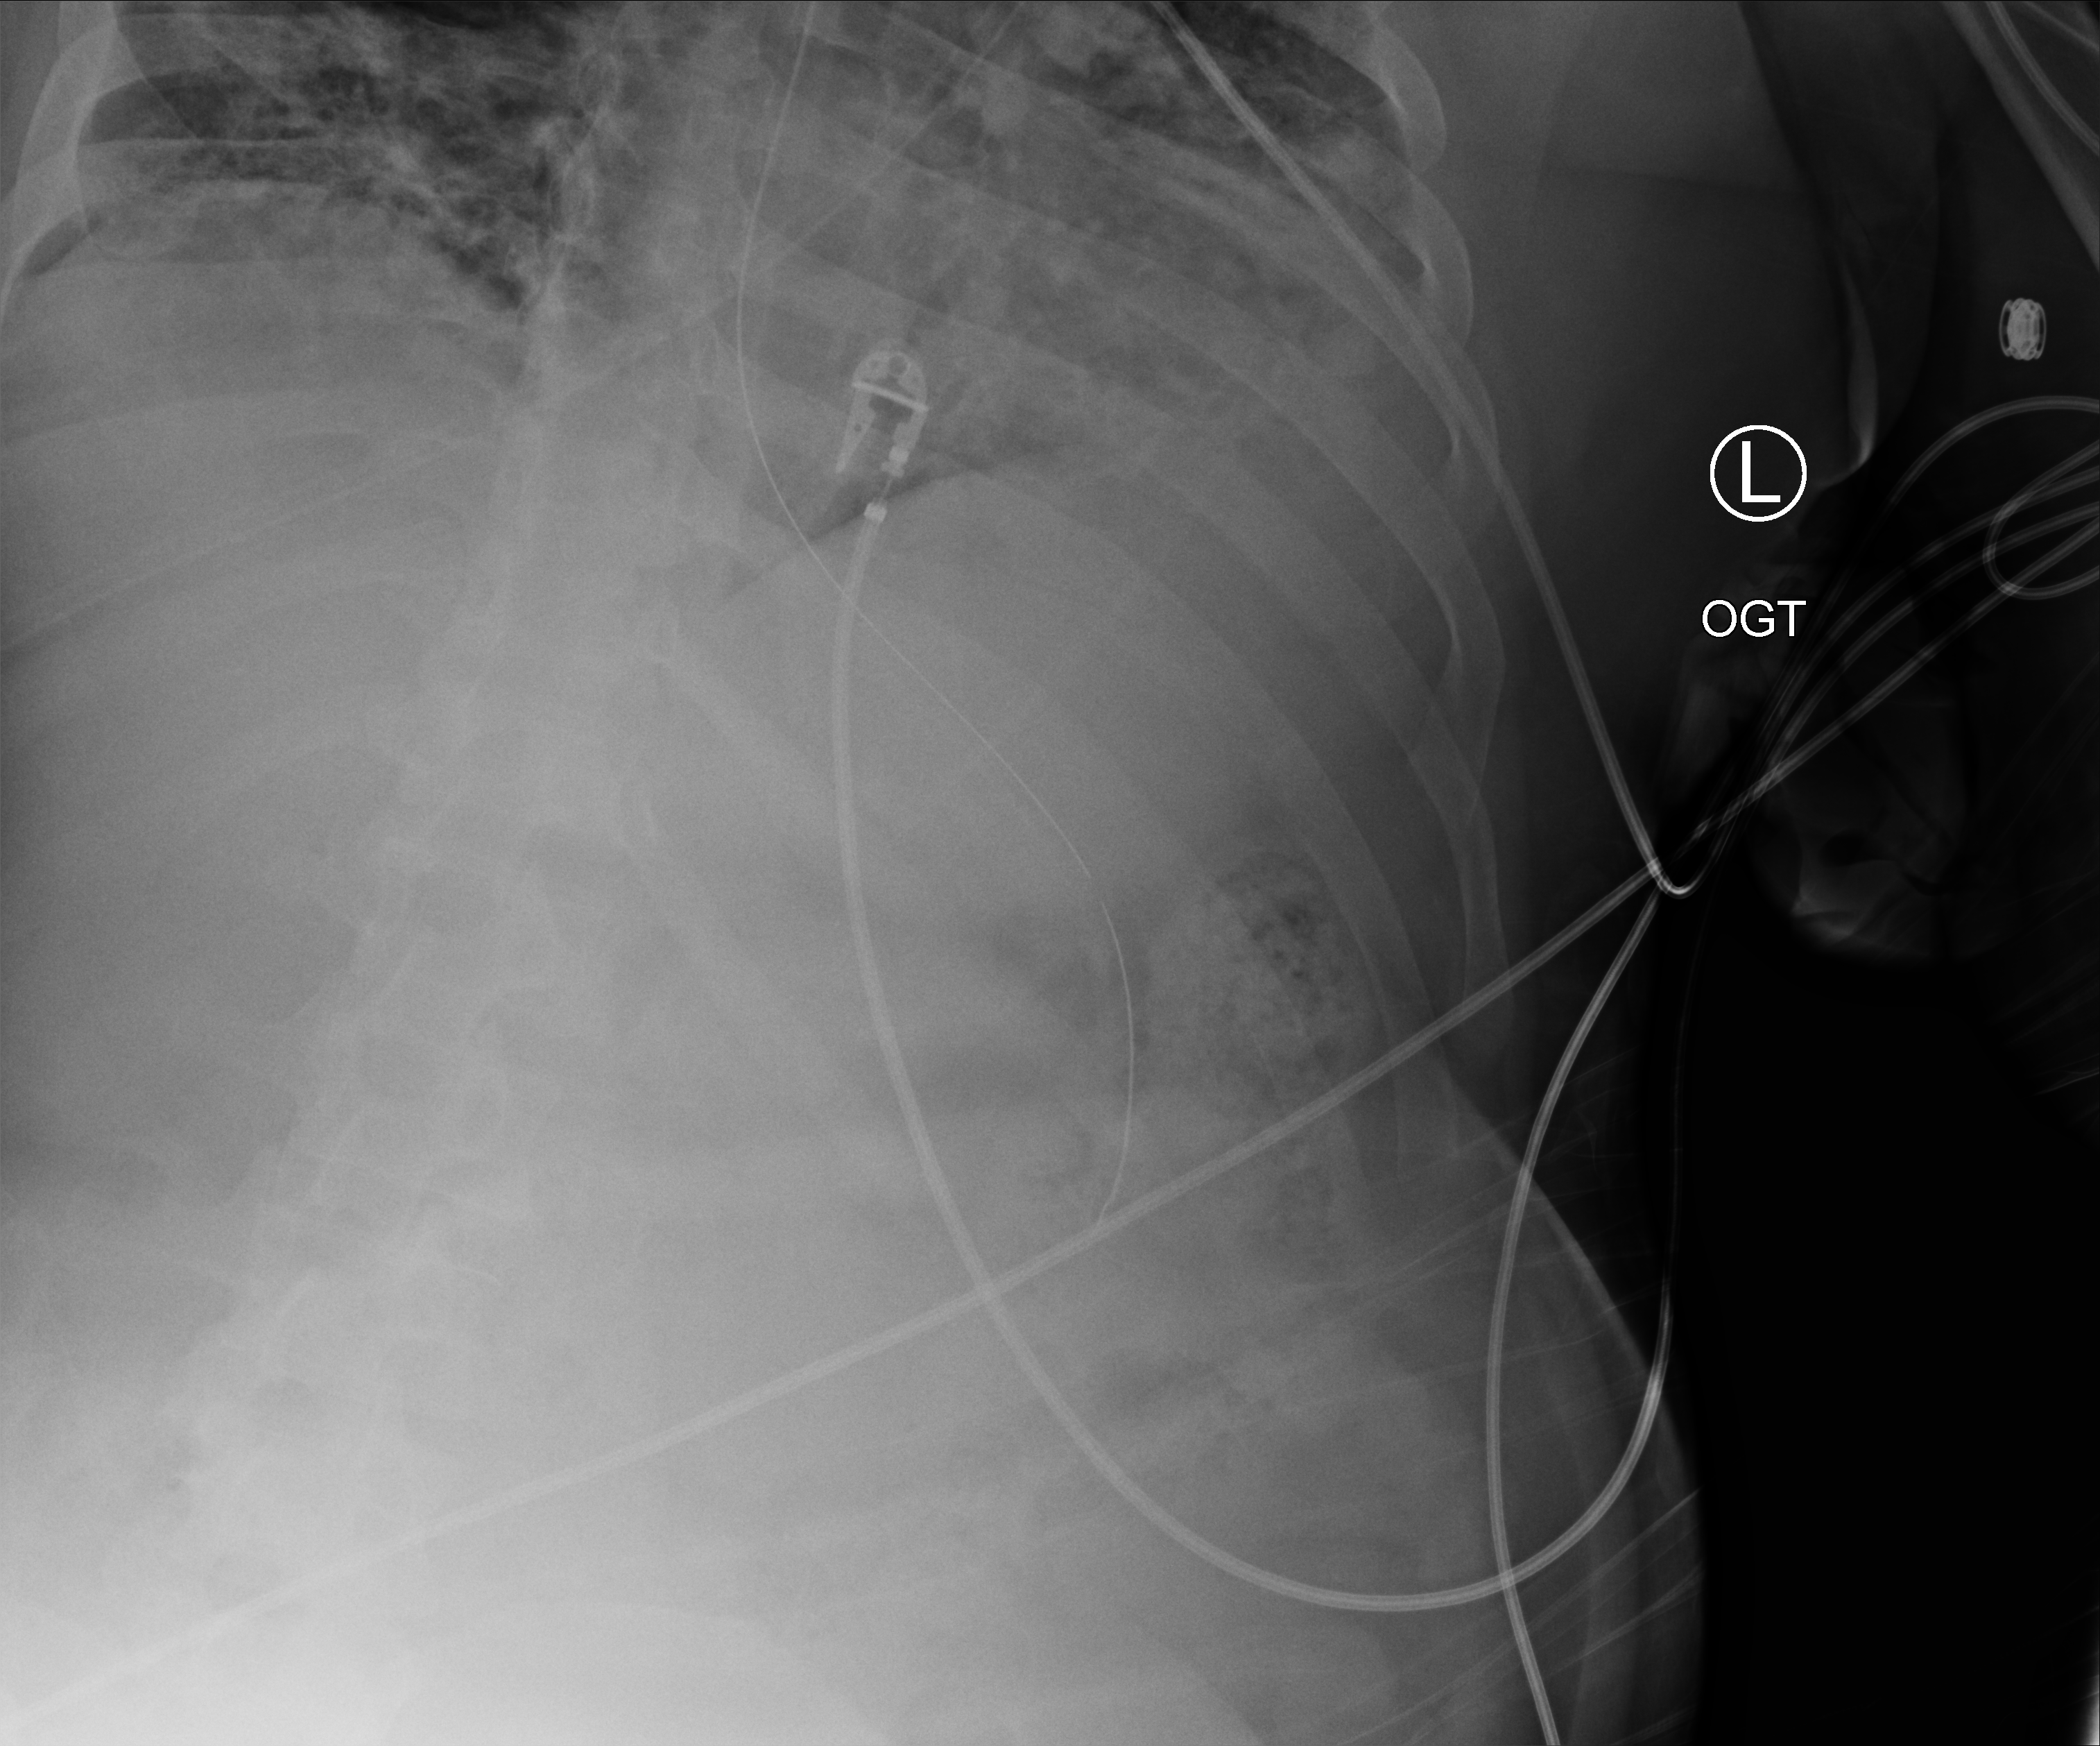
Bedside chest radiograph (computed radiography). Male patient hospitalised with COVID-19, age 18–59 years.
From the hospital-stay record, not from the radiograph (when in the stay this image was taken is not recorded):
- chronic kidney disease (admission record): yes
- length of hospital stay: 41 days